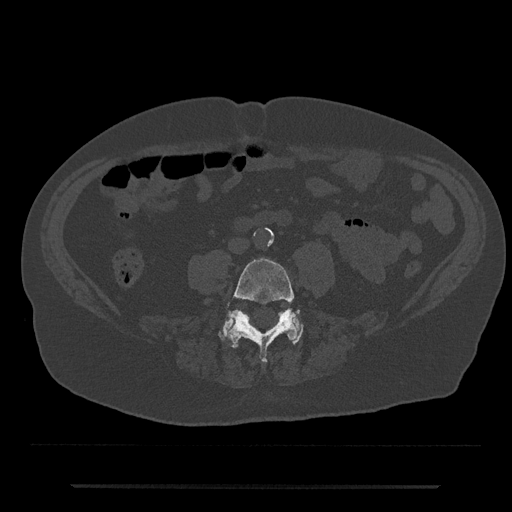
CT including the spine, one axial slice; slice 342 of 797 in the series (ordered by position); bone window (W 1800 / L 400 HU); 512 × 512 image matrix. Male patient, age 80 years. Case-level facts recorded for this patient, not image findings: primary cancer: prostate.
Annotated regions visible in this slice (semi-automatic segmentation, software-assisted and operator-edited):
- L4 vertebra: bounding box [x1, y1, x2, y2] px = [228, 258, 309, 363]
- L5 vertebra: [219, 315, 303, 344]